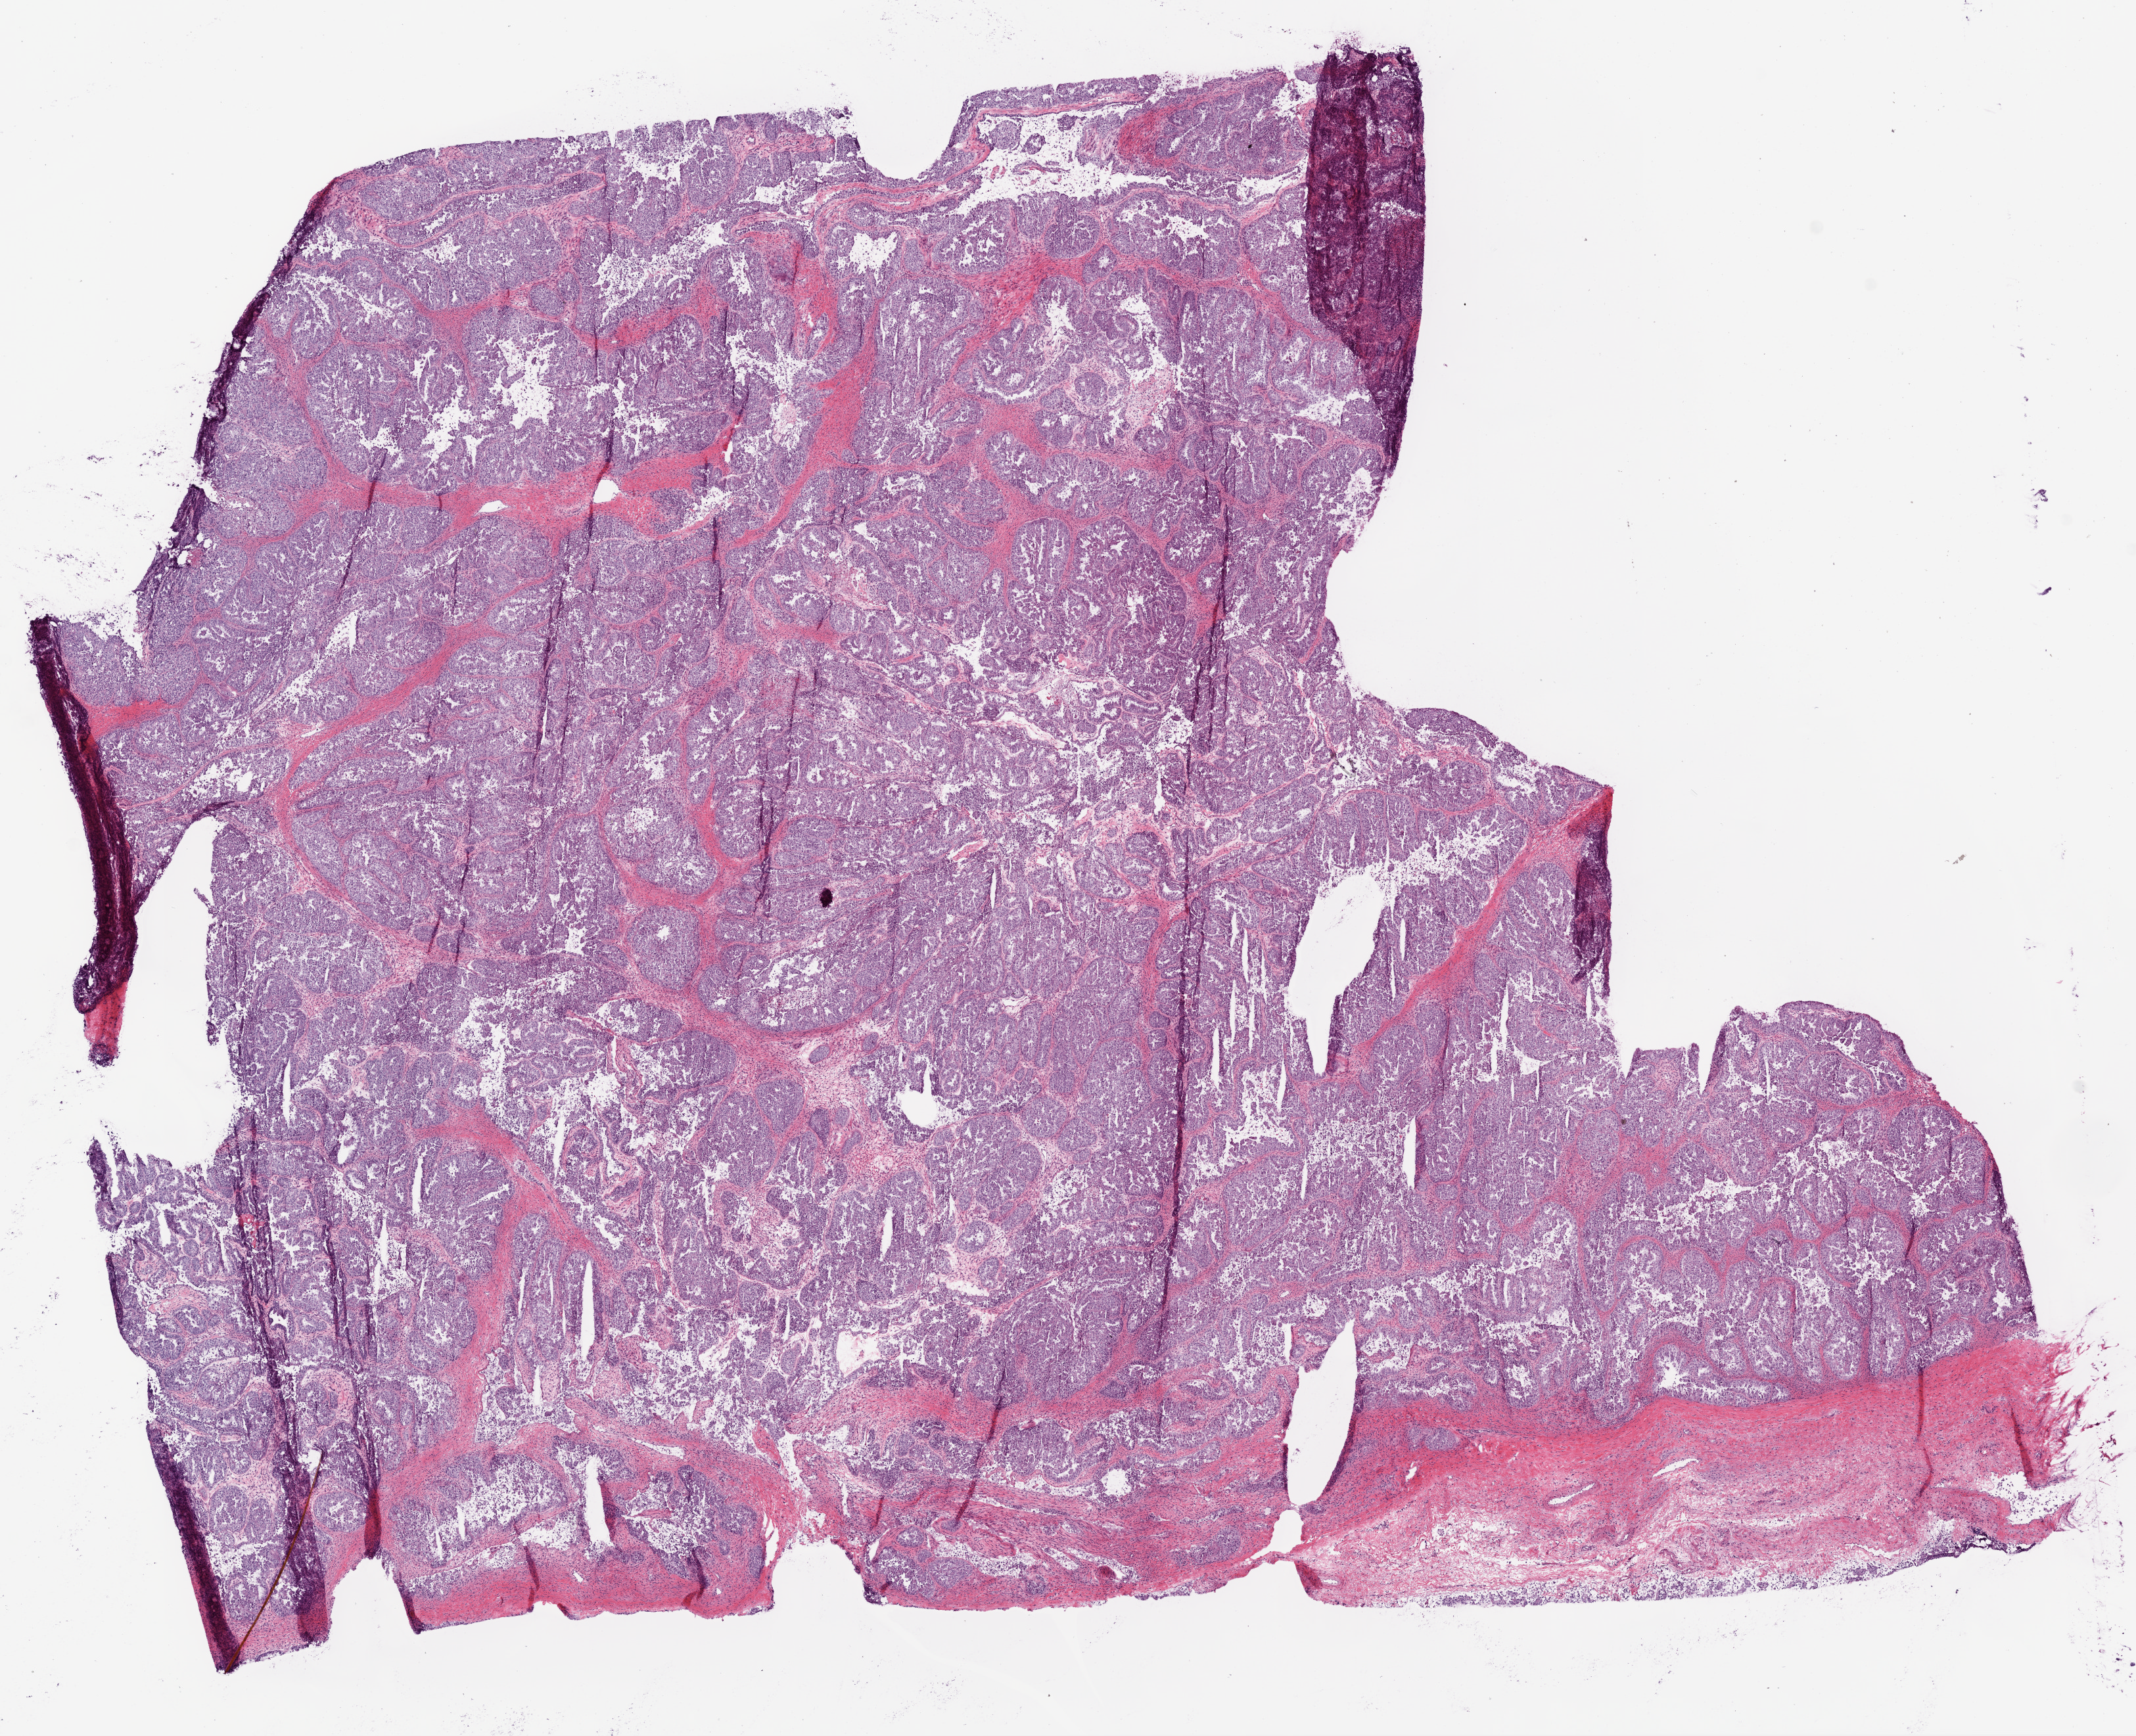
H&E whole-slide image, shown as a low-resolution overview of the whole scanned area (about 13.0 x 10.6 mm, from a 20x scan). Frozen section. Sample: primary tumour, ovary. Female, age 54 years at initial diagnosis. Histologic grade: G3 (poorly differentiated). Pathologist review of this section (percent, as recorded): tumour cells 80%, tumour nuclei 85%, normal cells 8%, stromal cells 12%, necrosis 8%.
Diagnosis: Serous cystadenocarcinoma, NOS. FIGO stage: IIC.